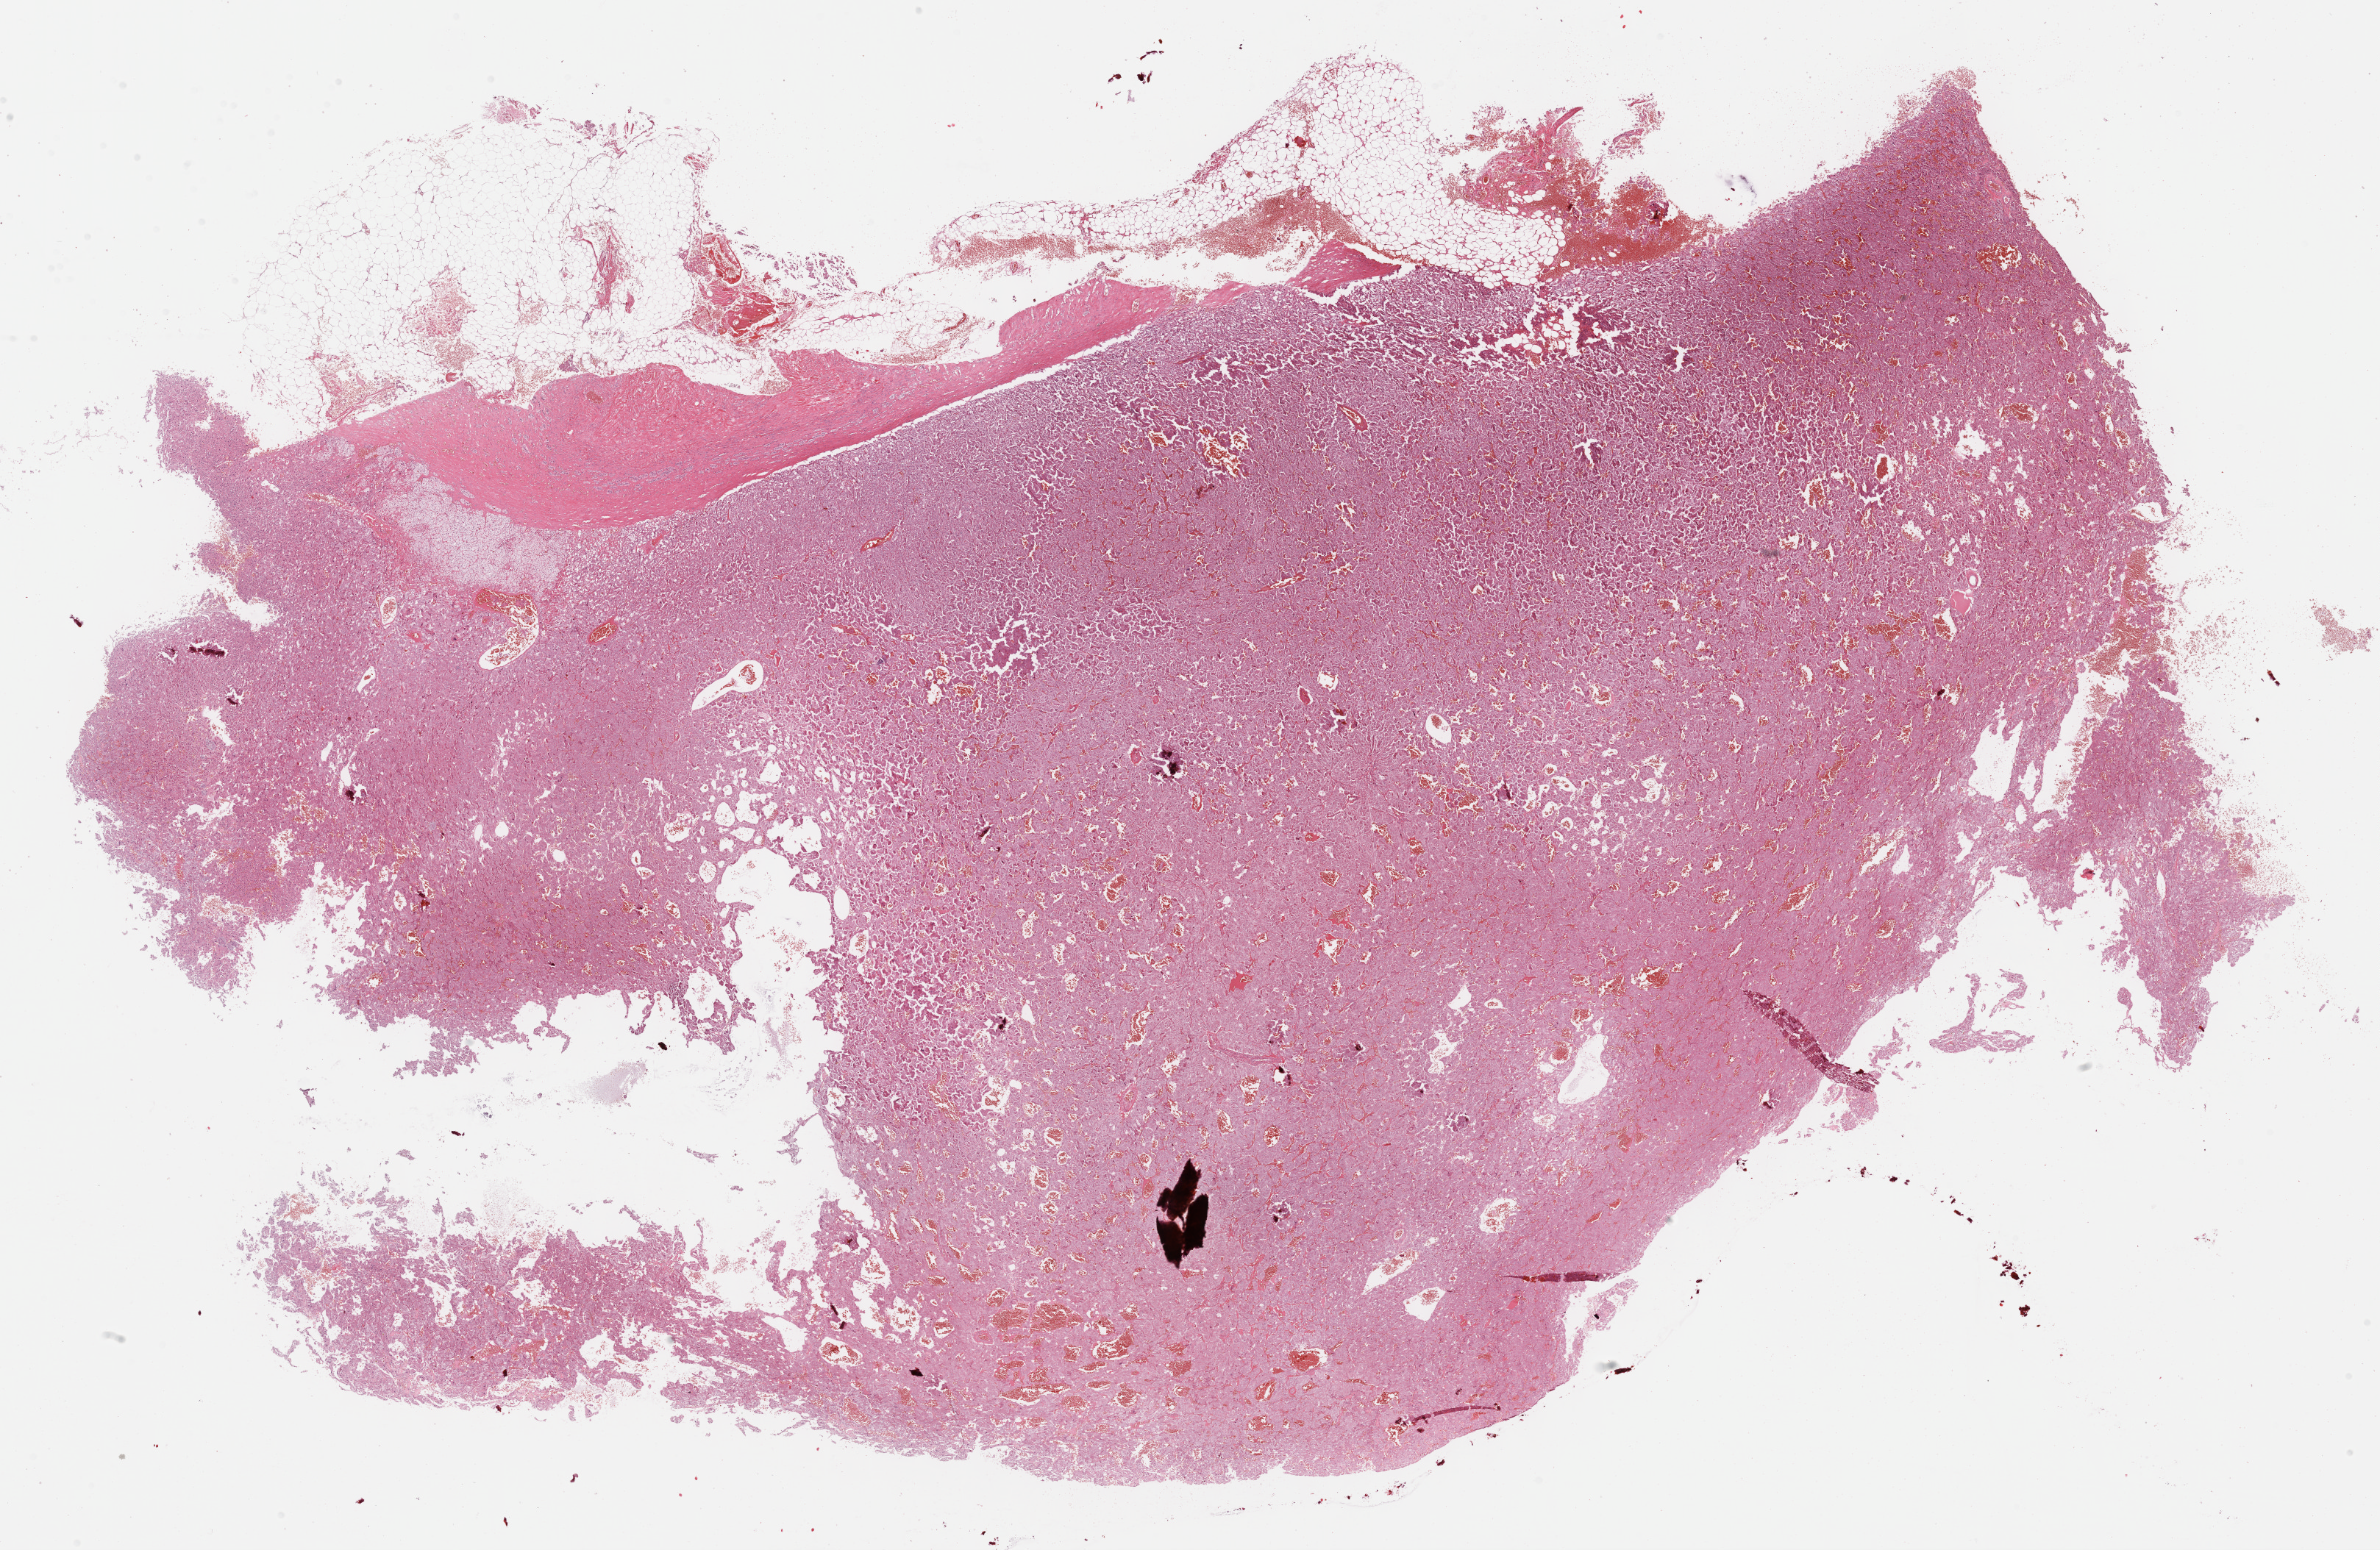
Hematoxylin and eosin (H&E) stained whole-slide image — shown as a low-resolution overview of the whole scanned area (about 26.2 x 17.1 mm). Formalin-fixed paraffin-embedded (FFPE) diagnostic section. Primary tumour sample from the adrenal gland. Female, age 57 years at initial diagnosis.
- pathologic diagnosis: Pheochromocytoma, NOS